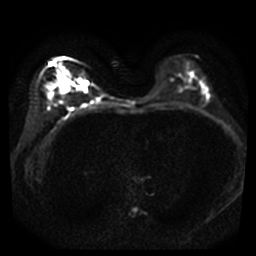
Breast MRI, one axial slice. Position 19 of 40 along the scan axis. Diffusion-weighted series; image 2 of 4 stored at this slice position (different b-values; order by instance number). 3 T. 5 mm slice thickness. 256 × 256 image matrix. Female patient.
Structures marked on this image (expert manual segmentation):
- tumour on diffusion-weighted imaging: bounding box [x1, y1, x2, y2] px = [51, 71, 68, 88]